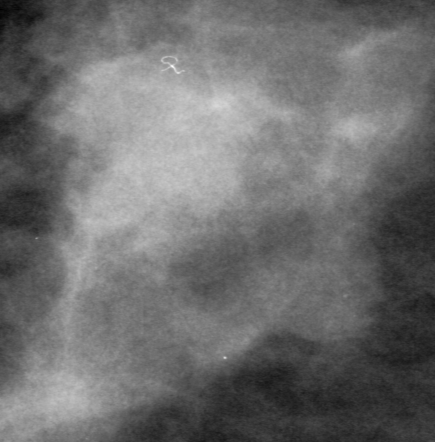
Cropped region of a digitized screen-film mammogram centred on a radiologist-marked abnormality; right breast; MLO view; BI-RADS breast density category 2 (scale 1–4).
Marked abnormality: mass, shape irregular, margins ill defined; BI-RADS assessment category 3; pathology result (as recorded, not read from the image): malignant.